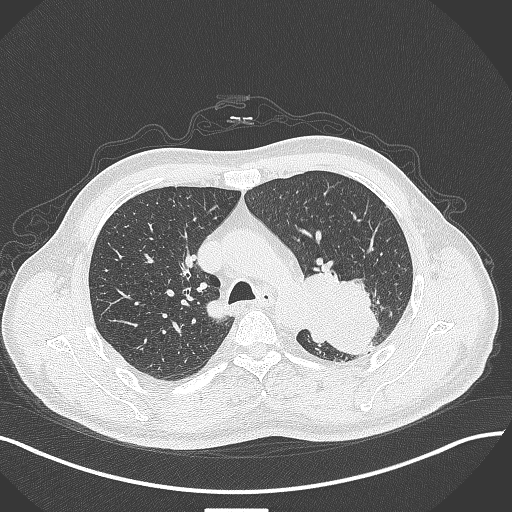
Chest CT, one axial slice; slice 298 of 429 in the series (ordered by position); lung window (W 1500 / L -600 HU); 1 mm slice thickness; 512 × 512 image matrix, field of view 400 × 400 mm. Patient: male, 55 years. Case-level facts recorded for this patient, not image findings: clinical TNM (as recorded): T3 N0 M1c; histopathological grade: G3.
Outlined on this slice (bounding box drawn by a radiologist):
- lung tumour (recorded histology: adenocarcinoma): bounding box <304,269,383,357> (left, top, right, bottom; pixels)